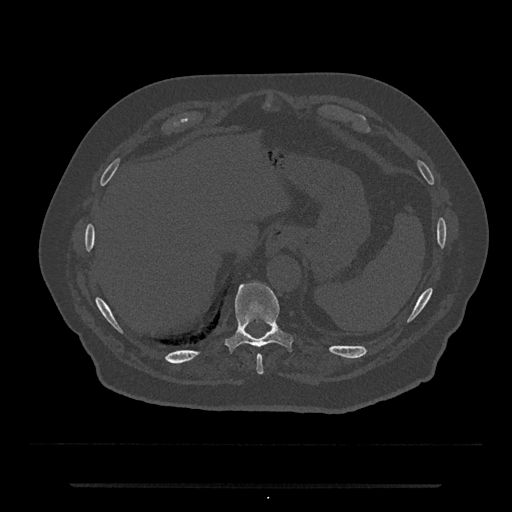
CT including the spine, one axial slice. Bone window (W 1800 / L 400 HU). 0.5 mm slice thickness. 512 × 512 image matrix, field of view 434 × 434 mm. Male patient, age 80 years. From the clinical record (not read from this slice): primary cancer: prostate; vertebrae with lytic lesions (as recorded): L1, T11.
Annotated regions visible in this slice (semi-automatically segmented with operator editing):
- T10 vertebra: bounding box (x1, y1, x2, y2) in pixels: (226, 283, 292, 351)
- T9 vertebra: (256, 355, 264, 375)